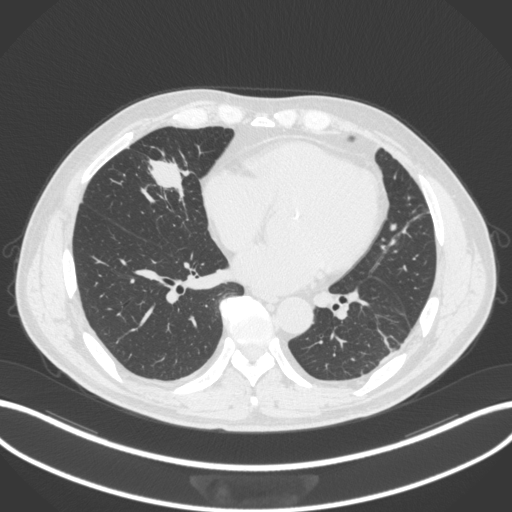
Chest CT, one axial slice; position 108 of 399 along the scan axis; reconstruction kernel B31f; lung window (W 1500 / L -600 HU); 1 mm slice thickness; 512 × 512 image matrix, field of view 400 × 400 mm. Patient: male, 59 years. From the clinical record (not read from this slice): clinical TNM (as recorded): T2a N1 M0.
Annotated regions visible in this slice (rectangle marked by the reading radiologist):
- lung tumour (recorded histology: adenocarcinoma): bounding box <142,148,198,206> (left, top, right, bottom; pixels)